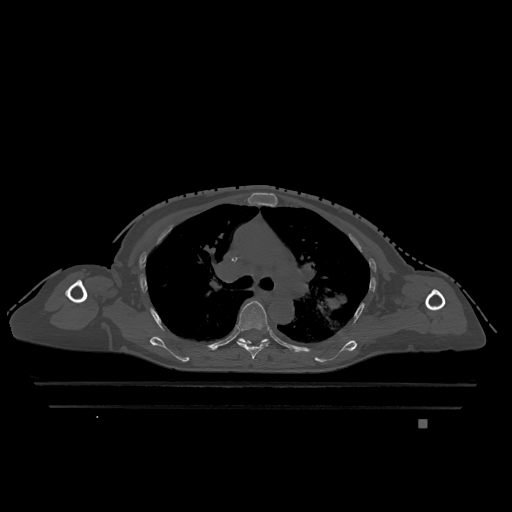
CT including the spine, one axial slice. Slice 823 of 1317 in the series (ordered by position). Bone window (W 1800 / L 400 HU). 0.5 mm slice thickness. 512 × 512 image matrix. Female patient, age 74 years. Case-level facts recorded for this patient, not image findings: primary cancer: lung; vertebrae with lytic lesions (as recorded): T1, T4, T5, T6, L4, L5.
Structures marked on this image (semi-automatic segmentation, software-assisted and operator-edited):
- T5 vertebra: bounding box (x1, y1, x2, y2) in pixels: (237, 301, 270, 360)
- T6 vertebra: (238, 338, 269, 344)